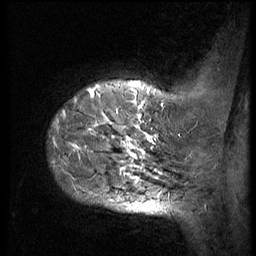
Breast MRI (dynamic contrast-enhanced), one sagittal slice; slice 9 of 56 in the series (ordered by position); 3 images stored at this slice position (order not interpretable as contrast timing); 1.5 T; TE 4.2 ms, TR 9 ms; 256 × 256 image matrix, field of view 180 × 180 mm. Female patient, age 49 years. From the clinical record (not read from this slice): setting: breast cancer imaged before/during neoadjuvant chemotherapy; receptor status: HER2-positive.
Outlined on this slice (semi-automatic segmentation, software-assisted and operator-edited):
- analysis volume of interest (the breast-tissue region the enhancement analysis was run in; not a lesion): box from (x=46, y=85) to (x=168, y=207) px
- tumour enhancement mask (voxels above the 140 % enhancement threshold inside the analysis volume of interest): (x=52, y=87)–(x=164, y=204)